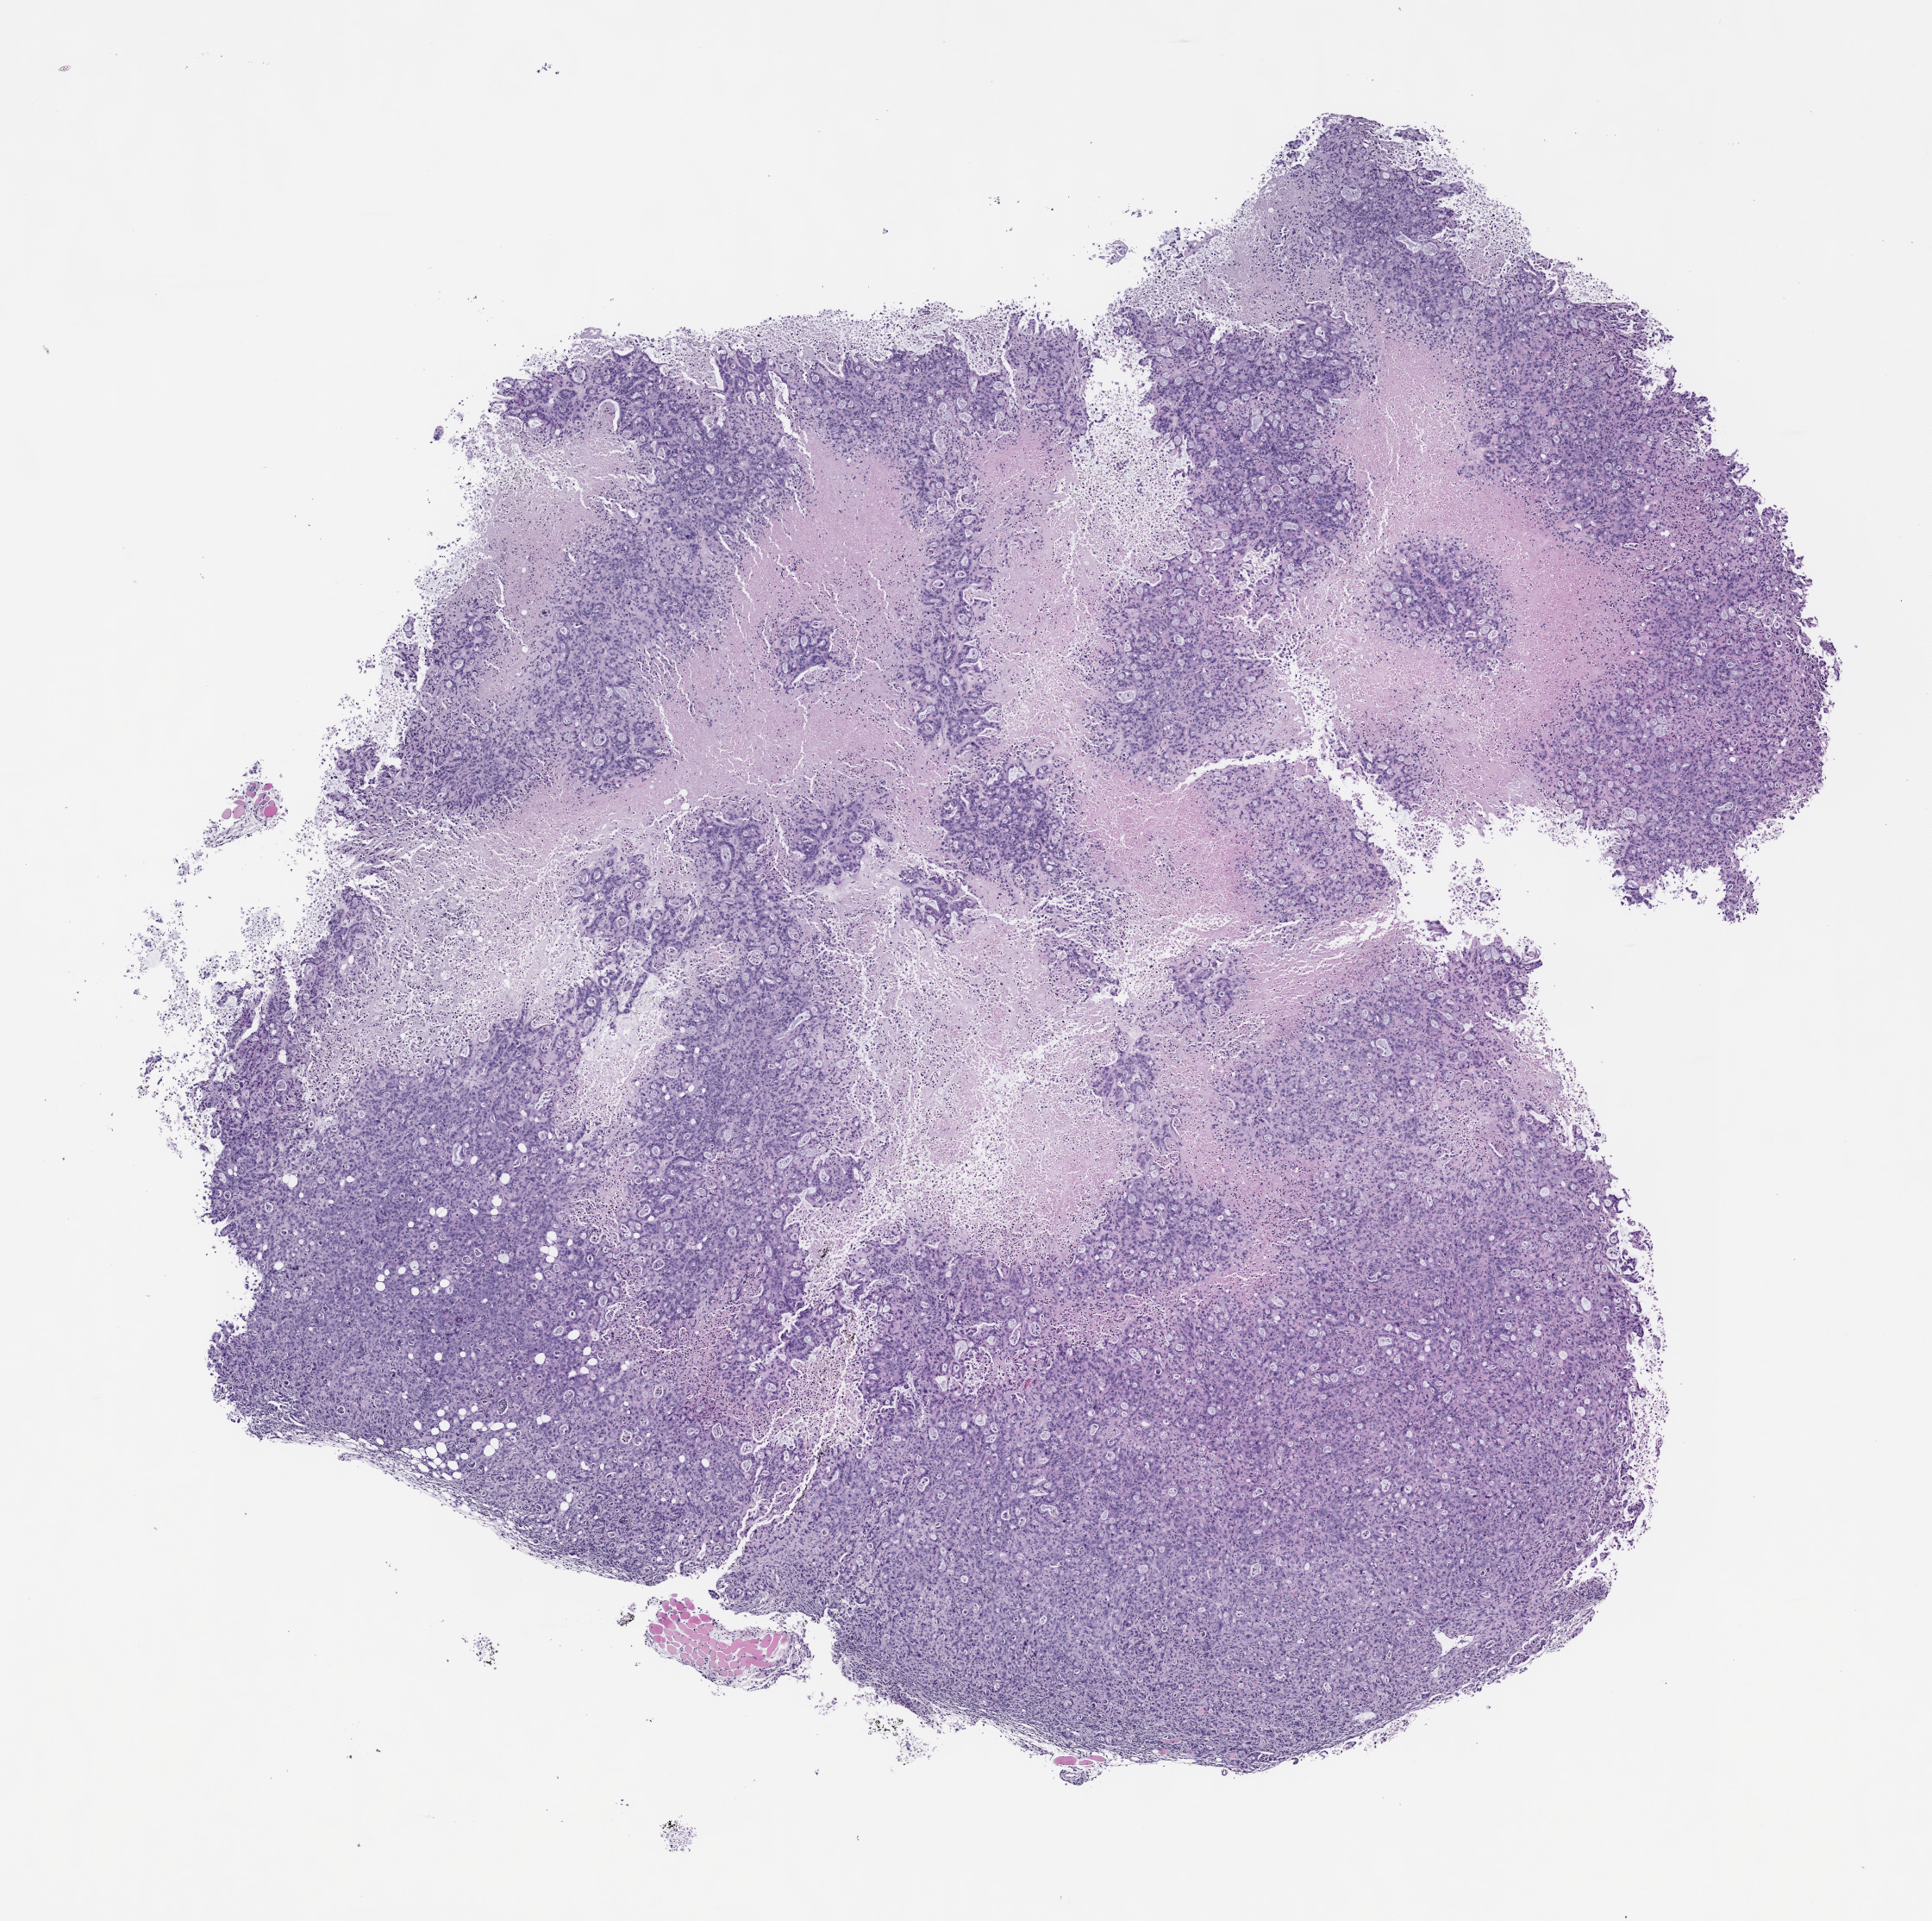
Whole-slide image, H&E: patient-derived xenograft (human tumor grown in a mouse) — whole scanned area (about 9.0 x 9.0 mm) shown as a low-resolution overview. Formalin-fixed paraffin-embedded section. Originating tumor site category: pancreas.
Originating patient diagnosis: Pancreatic Adenocarcinoma.